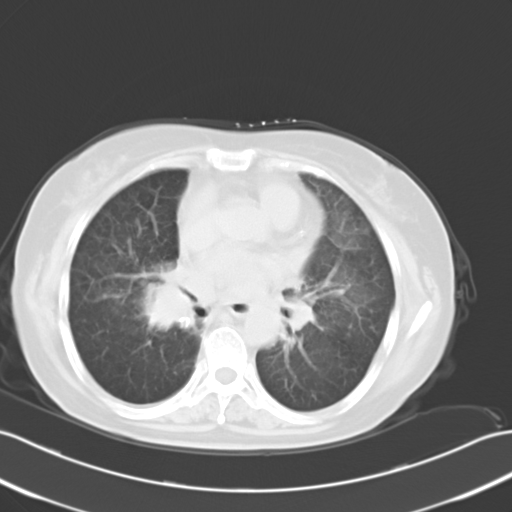
Chest CT, one axial slice. Position 17 of 30 along the scan axis. 120 kVp. Lung window (W 1500 / L -600 HU). 512 × 512 image matrix, field of view 353 × 353 mm. Patient: female, 65 years. Case-level facts recorded for this patient, not image findings: clinical TNM (as recorded): T1c N3 M0.
Annotated regions visible in this slice (rectangle marked by the reading radiologist):
- lung tumour (recorded histology: small cell carcinoma): bounding box [x1, y1, x2, y2] px = [137, 274, 201, 345]